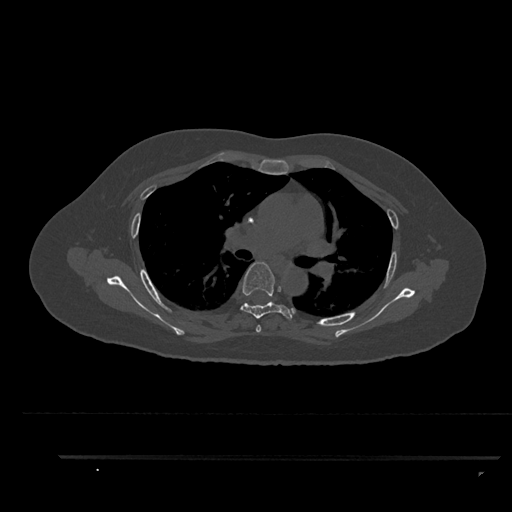
CT including the spine, one axial slice. Slice 603 of 797 in the series (ordered by position). Reconstruction kernel Br40s/3. 120 kVp. Bone window (W 1800 / L 400 HU). 0.5 mm slice thickness. 512 × 512 image matrix. Patient: female, 44 years. From the clinical record (not read from this slice): primary cancer: renal; vertebrae with lytic lesions (as recorded): L1.
Annotated regions visible in this slice (semi-automatic segmentation, software-assisted and operator-edited):
- T4 vertebra: bounding box (x1, y1, x2, y2) in pixels: (256, 325, 261, 333)
- T5 vertebra: (240, 262, 292, 320)
- T6 vertebra: (264, 303, 268, 306)